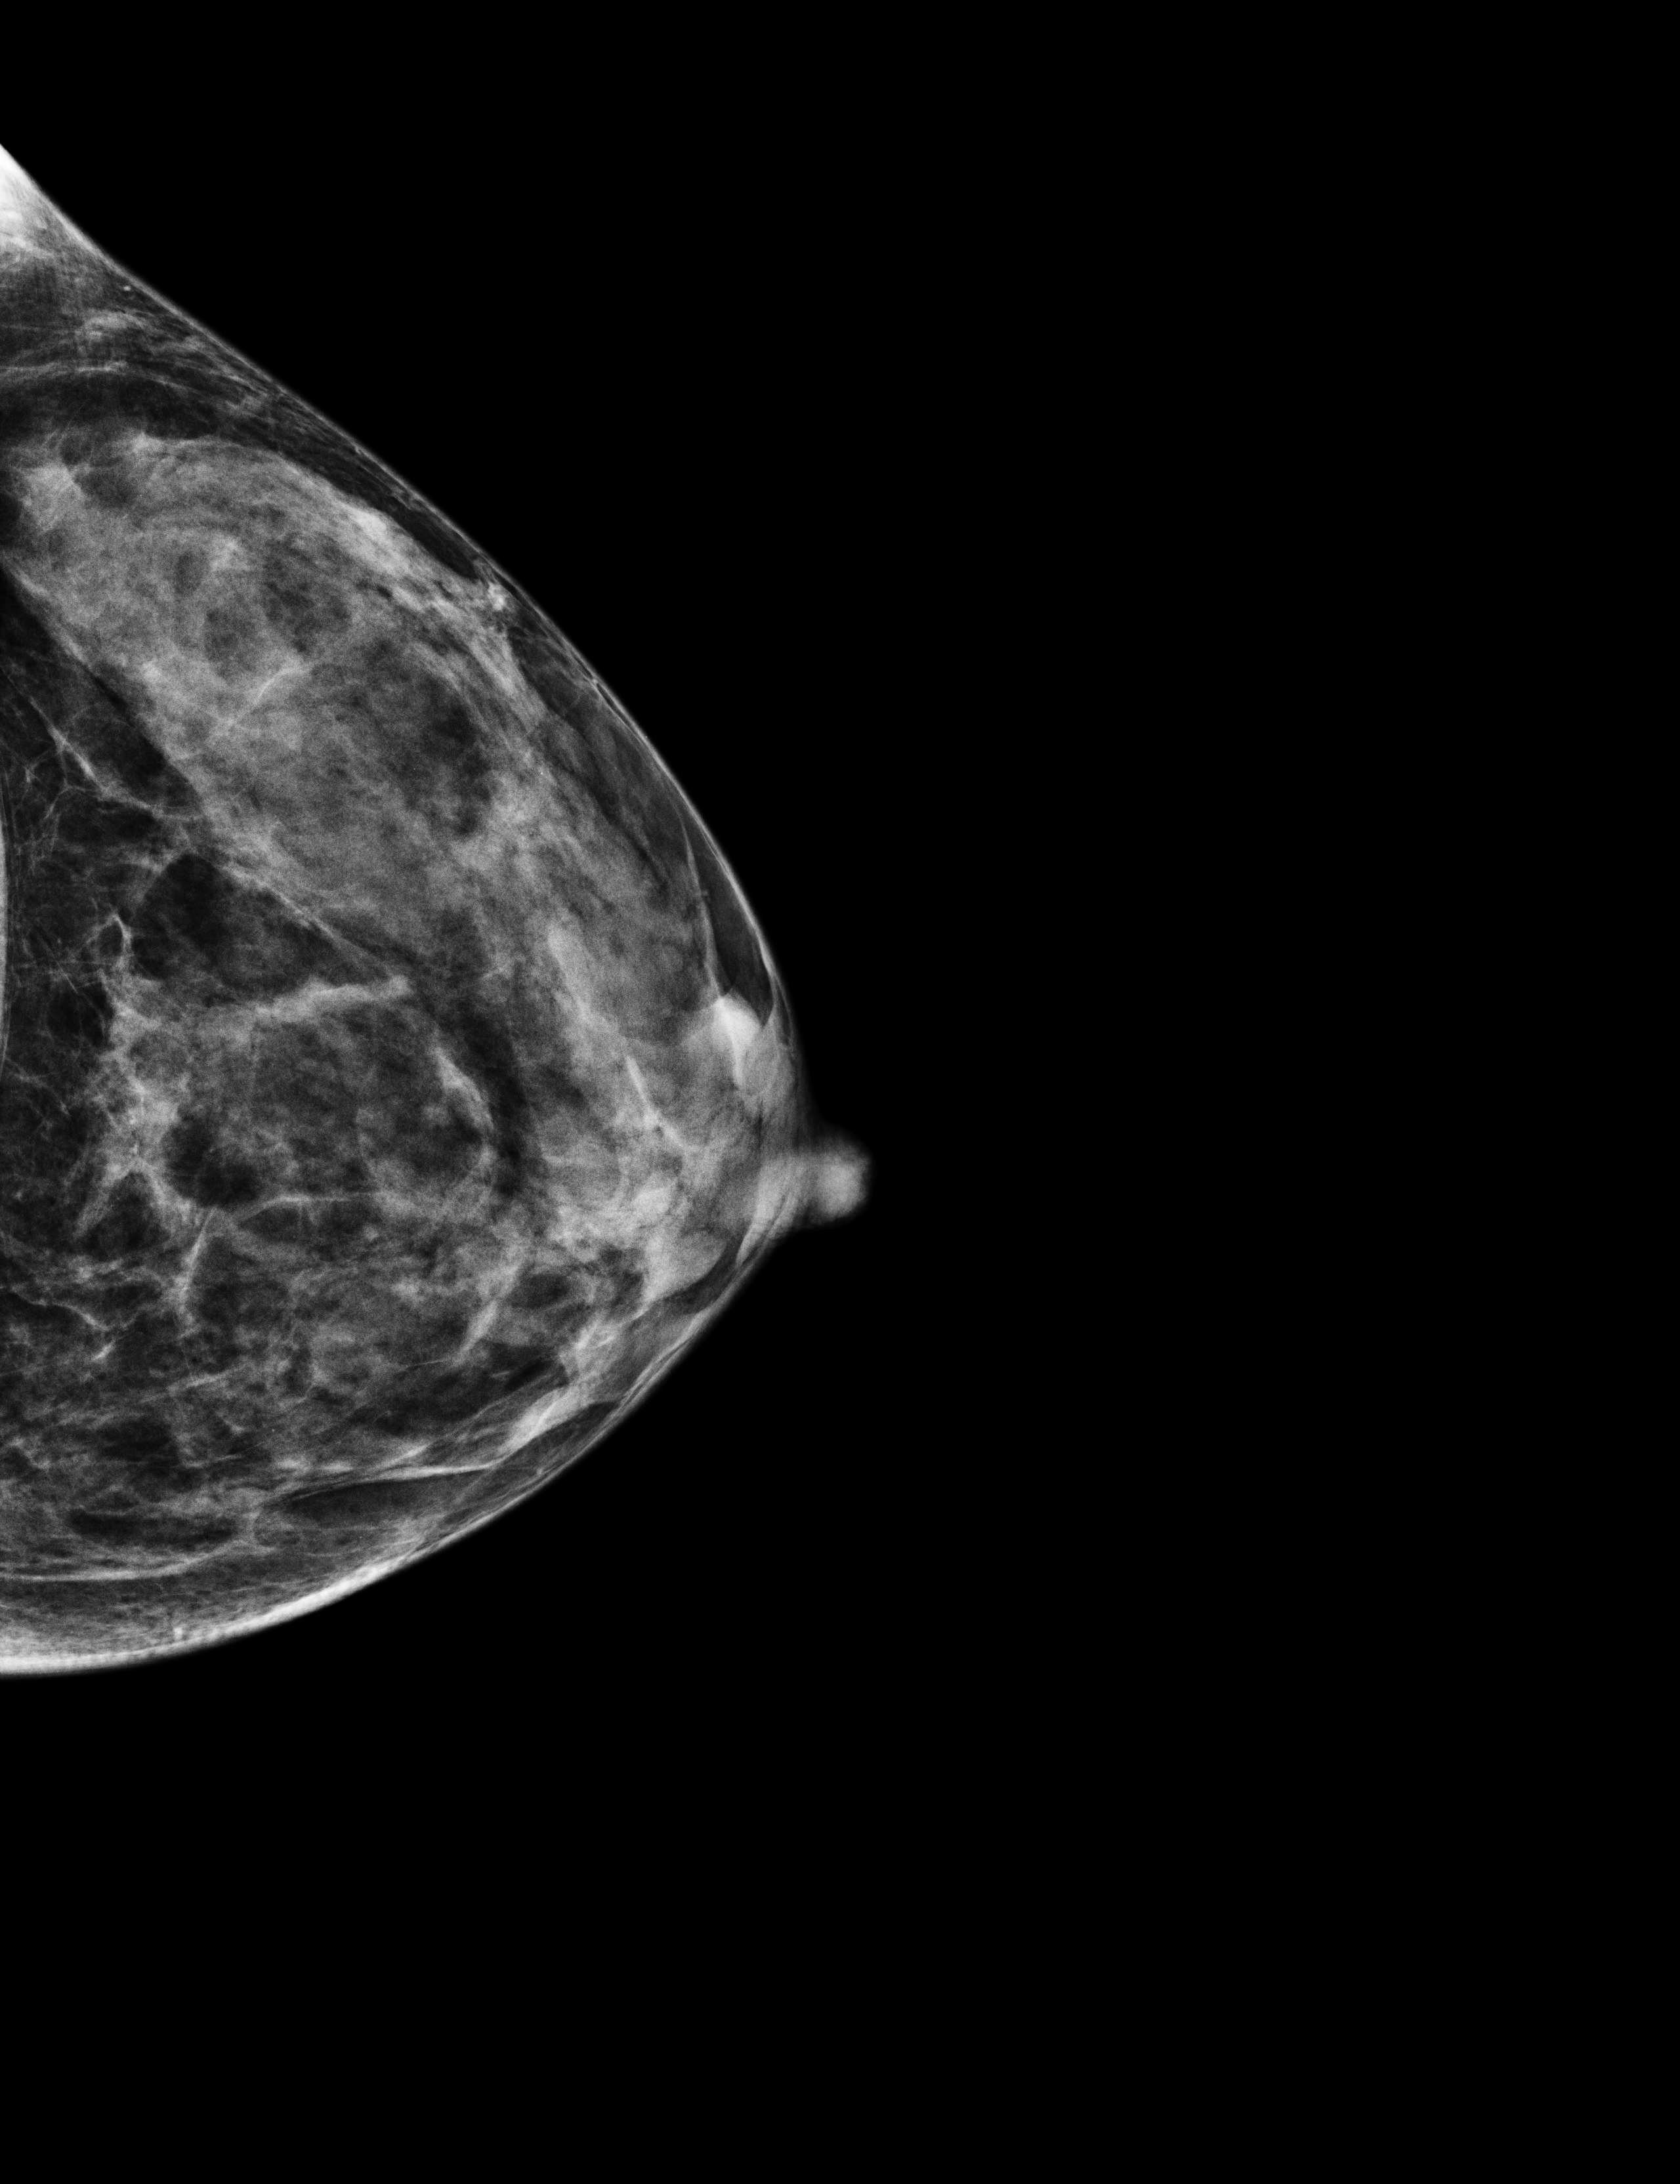
Full-field digital mammogram (FFDM); left breast; craniocaudal (CC) view; annual screening mammography examination. Female patient, age 55 years.
Final BI-RADS category for the screening round (tomosynthesis exam, both breasts): category 2.